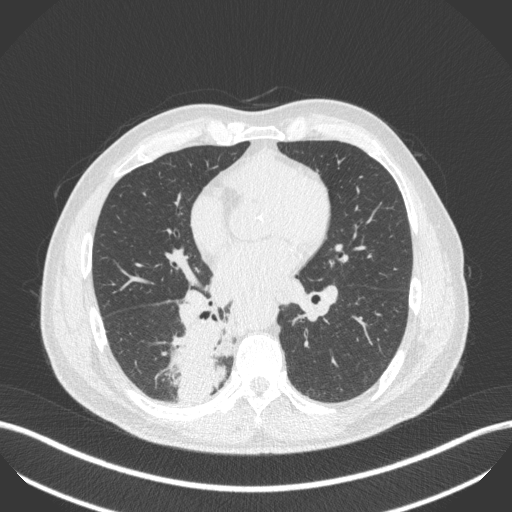
Chest CT, one axial slice. Position 224 of 451 along the scan axis. Reconstruction kernel B31f. 100 kVp. Lung window (W 1500 / L -600 HU). 1 mm slice thickness. 512 × 512 image matrix. Patient: male, 61 years. Case-level facts recorded for this patient, not image findings: clinical TNM (as recorded): T1 N0 M0; histopathological grade: G3.
Structures marked on this image (rectangle marked by the reading radiologist):
- lung tumour (recorded histology: small cell carcinoma): bounding box [x1, y1, x2, y2] px = [165, 305, 231, 403]